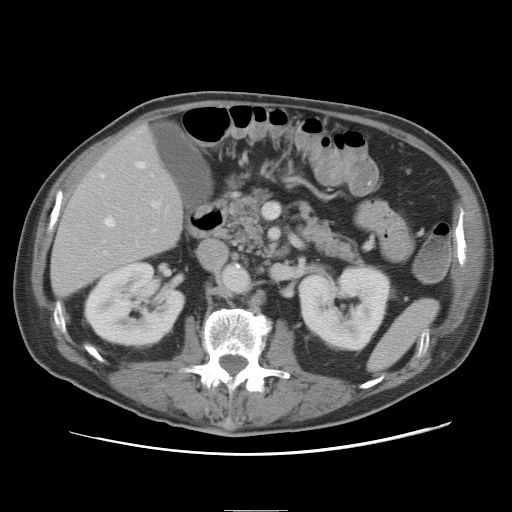
Contrast-enhanced abdominal CT, one axial slice; slice 30 of 89 in the series (ordered by position); 120 kVp; intravenous contrast given; soft-tissue window (W 400 / L 40 HU); 512 × 512 image matrix, field of view 375 × 375 mm. Male patient, age 69 years. From the clinical record (not read from this slice): diagnosis: colorectal cancer liver metastases, imaged before liver resection; multiple liver metastases: no; largest metastasis: 8.5 cm; disease in both lobes: no.
Outlined on this slice (expert manual segmentation):
- hepatic veins: bounding box <101,161,146,226> (left, top, right, bottom; pixels)
- liver: <52,125,182,297>
- planned liver remnant (the part of the liver to remain after resection): <52,125,182,297>
- portal vein (with intrahepatic branches): <105,200,160,253>